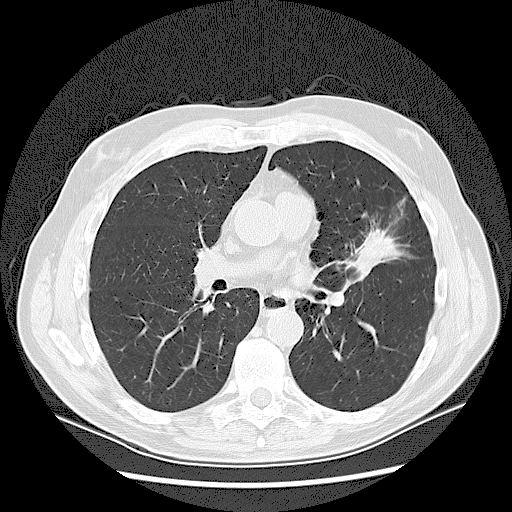
Low-dose screening chest CT, one axial slice. Position 71 of 132 along the scan axis. Lung window (W 1500 / L -600 HU). 512 × 512 image matrix, field of view 380 × 380 mm.
Outlined on this slice (expert manual segmentation):
- lesion 1 (tumor, upper lobe of left lung): bounding box (x1, y1, x2, y2) in pixels: (357, 230, 398, 272)